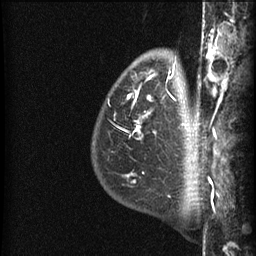
Breast MRI (dynamic contrast-enhanced), one sagittal slice. Dynamic contrast-enhanced series, image 2 of 3 at this slice position (ordered by acquisition). 1.5 T. TE 4.2 ms, TR 22.7 ms. 1.5 mm slice thickness. 256 × 256 image matrix, field of view 180 × 180 mm. Female patient, age 48 years. Case-level facts recorded for this patient, not image findings: setting: breast cancer imaged before/during neoadjuvant chemotherapy; receptor status: triple-negative.
Outlined on this slice (semi-automatic segmentation, software-assisted and operator-edited):
- analysis volume of interest (the breast-tissue region the enhancement analysis was run in; not a lesion): bounding box (x1, y1, x2, y2) in pixels: (92, 48, 191, 180)
- tumour enhancement mask (voxels above the 90 % enhancement threshold inside the analysis volume of interest): (127, 72, 175, 137)